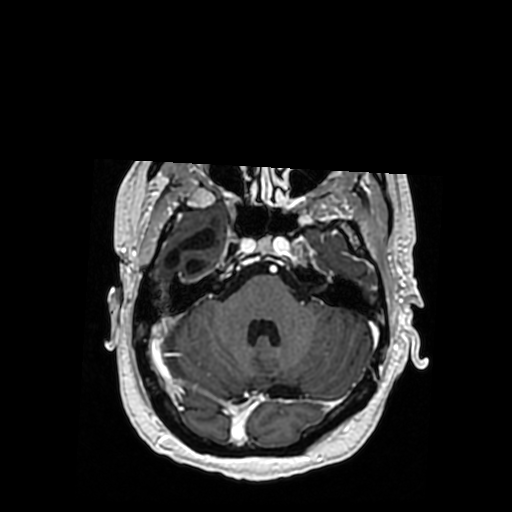
Brain MRI from a brain-tumour surgery series, one axial slice; slice 252 of 364 in the series (ordered by position); T1-weighted post-contrast; 512 × 512 image matrix, field of view 260 × 260 mm. From the clinical record (not read from this slice): histopathology: Oligodendroglioma; WHO grade: 3; IDH mutation: yes.
Structures marked on this image (manually delineated by an expert):
- previous resection cavity: bounding box (x1, y1, x2, y2) in pixels: (164, 229, 216, 274)